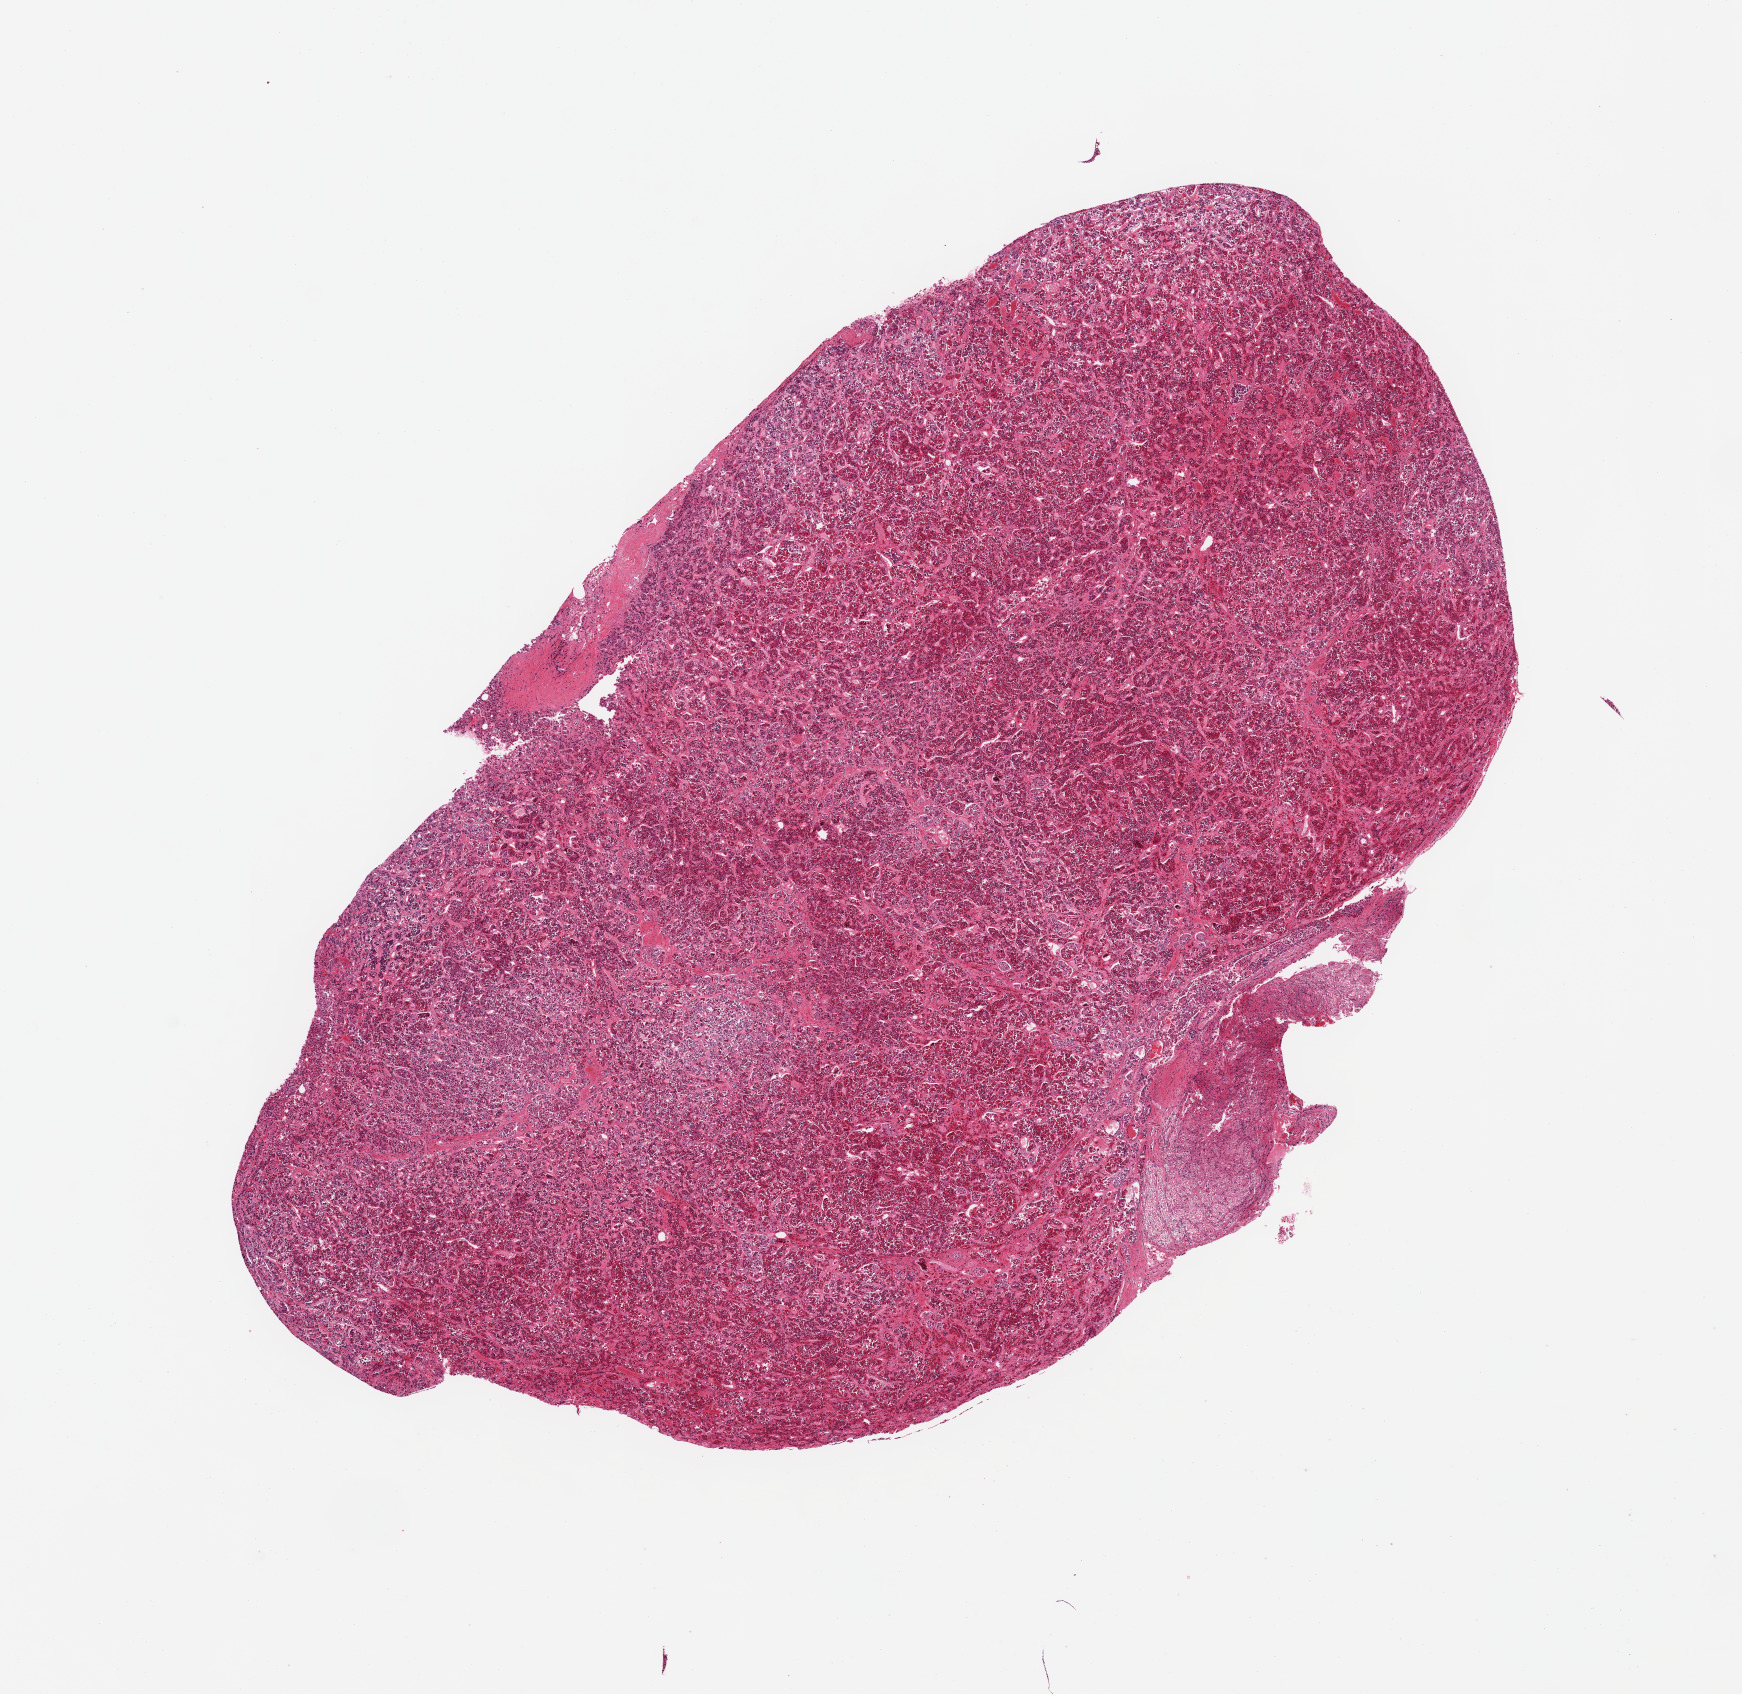
Whole-slide image, H&E stain, brightfield — low-resolution overview of the scanned area, about 13.8 x 13.4 mm; PAXgene-fixed paraffin-embedded (PFPE) section; target tissue: pituitary; tissue donor sample. Donor sex: male.
- reviewer comment on this tissue sample: 1 piece; mostly anterior lobe; posterior labeled